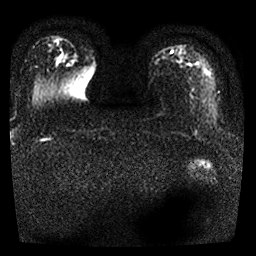
Breast MRI, one axial slice. Slice 4 of 25 in the series (ordered by position). Diffusion-weighted series; image 2 of 4 stored at this slice position (different b-values; order by instance number). 1.5 T. 4 mm slice thickness. 256 × 256 image matrix, field of view 290 × 290 mm. Female patient.
Outlined on this slice (expert manual segmentation):
- tumour on diffusion-weighted imaging: bounding box <55,58,67,64> (left, top, right, bottom; pixels)